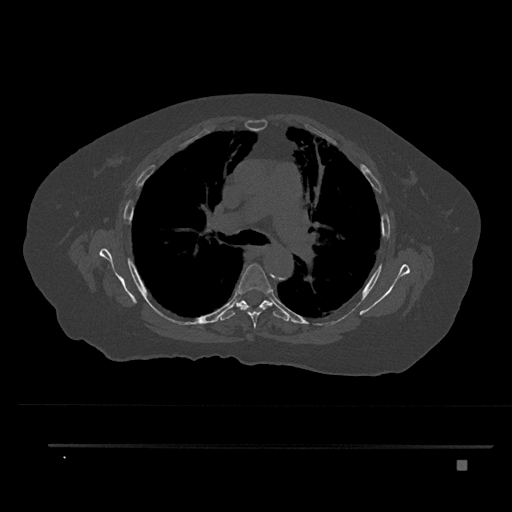
CT including the spine, one axial slice; position 551 of 797 along the scan axis; 120 kVp; bone window (W 1800 / L 400 HU); 0.5 mm slice thickness; 512 × 512 image matrix, field of view 437 × 437 mm. Female patient, age 76 years. Case-level facts recorded for this patient, not image findings: primary cancer: lung; vertebrae with lytic lesions (as recorded): T11, L3.
Structures marked on this image (semi-automatic segmentation, software-assisted and operator-edited):
- T5 vertebra: box from (x=236, y=263) to (x=271, y=328) px
- T6 vertebra: (x=219, y=300)–(x=290, y=321)